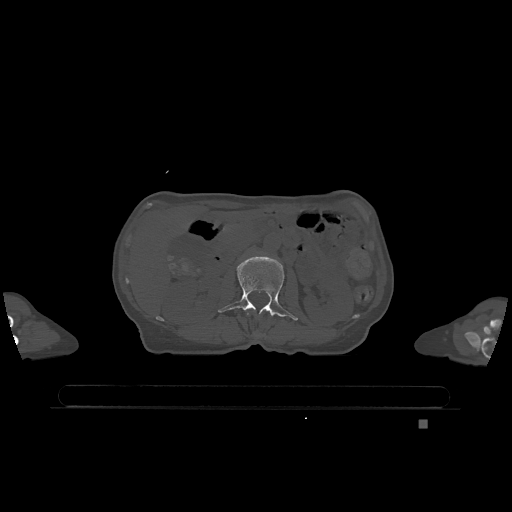
CT including the spine, one axial slice. Position 419 of 1317 along the scan axis. Bone window (W 1800 / L 400 HU). 512 × 512 image matrix, field of view 500 × 500 mm. Female patient, age 74 years. From the clinical record (not read from this slice): primary cancer: lung; vertebrae with lytic lesions (as recorded): T1, T4, T5, T6, L4, L5.
Outlined on this slice (semi-automatically segmented with operator editing):
- L2 vertebra: box from (x=218, y=256) to (x=298, y=321) px